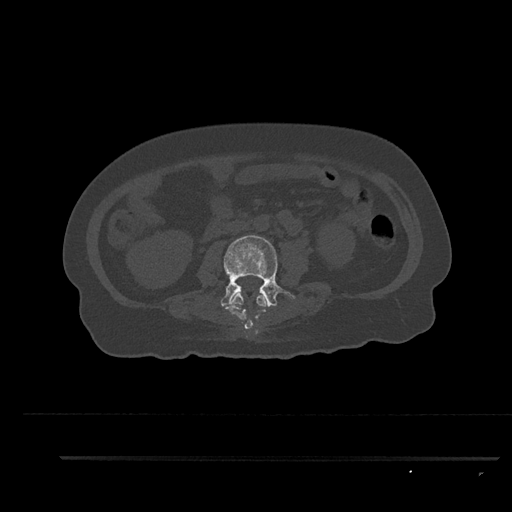
CT including the spine, one axial slice. Position 108 of 797 along the scan axis. Reconstruction kernel Br40s/3. 120 kVp. Bone window (W 1800 / L 400 HU). 0.5 mm slice thickness. 512 × 512 image matrix. Patient: female, 44 years. Case-level facts recorded for this patient, not image findings: primary cancer: renal.
Annotated regions visible in this slice (semi-automatically segmented with operator editing):
- L2 vertebra: bounding box (x1, y1, x2, y2) in pixels: (226, 293, 266, 329)
- L3 vertebra: (220, 235, 296, 312)